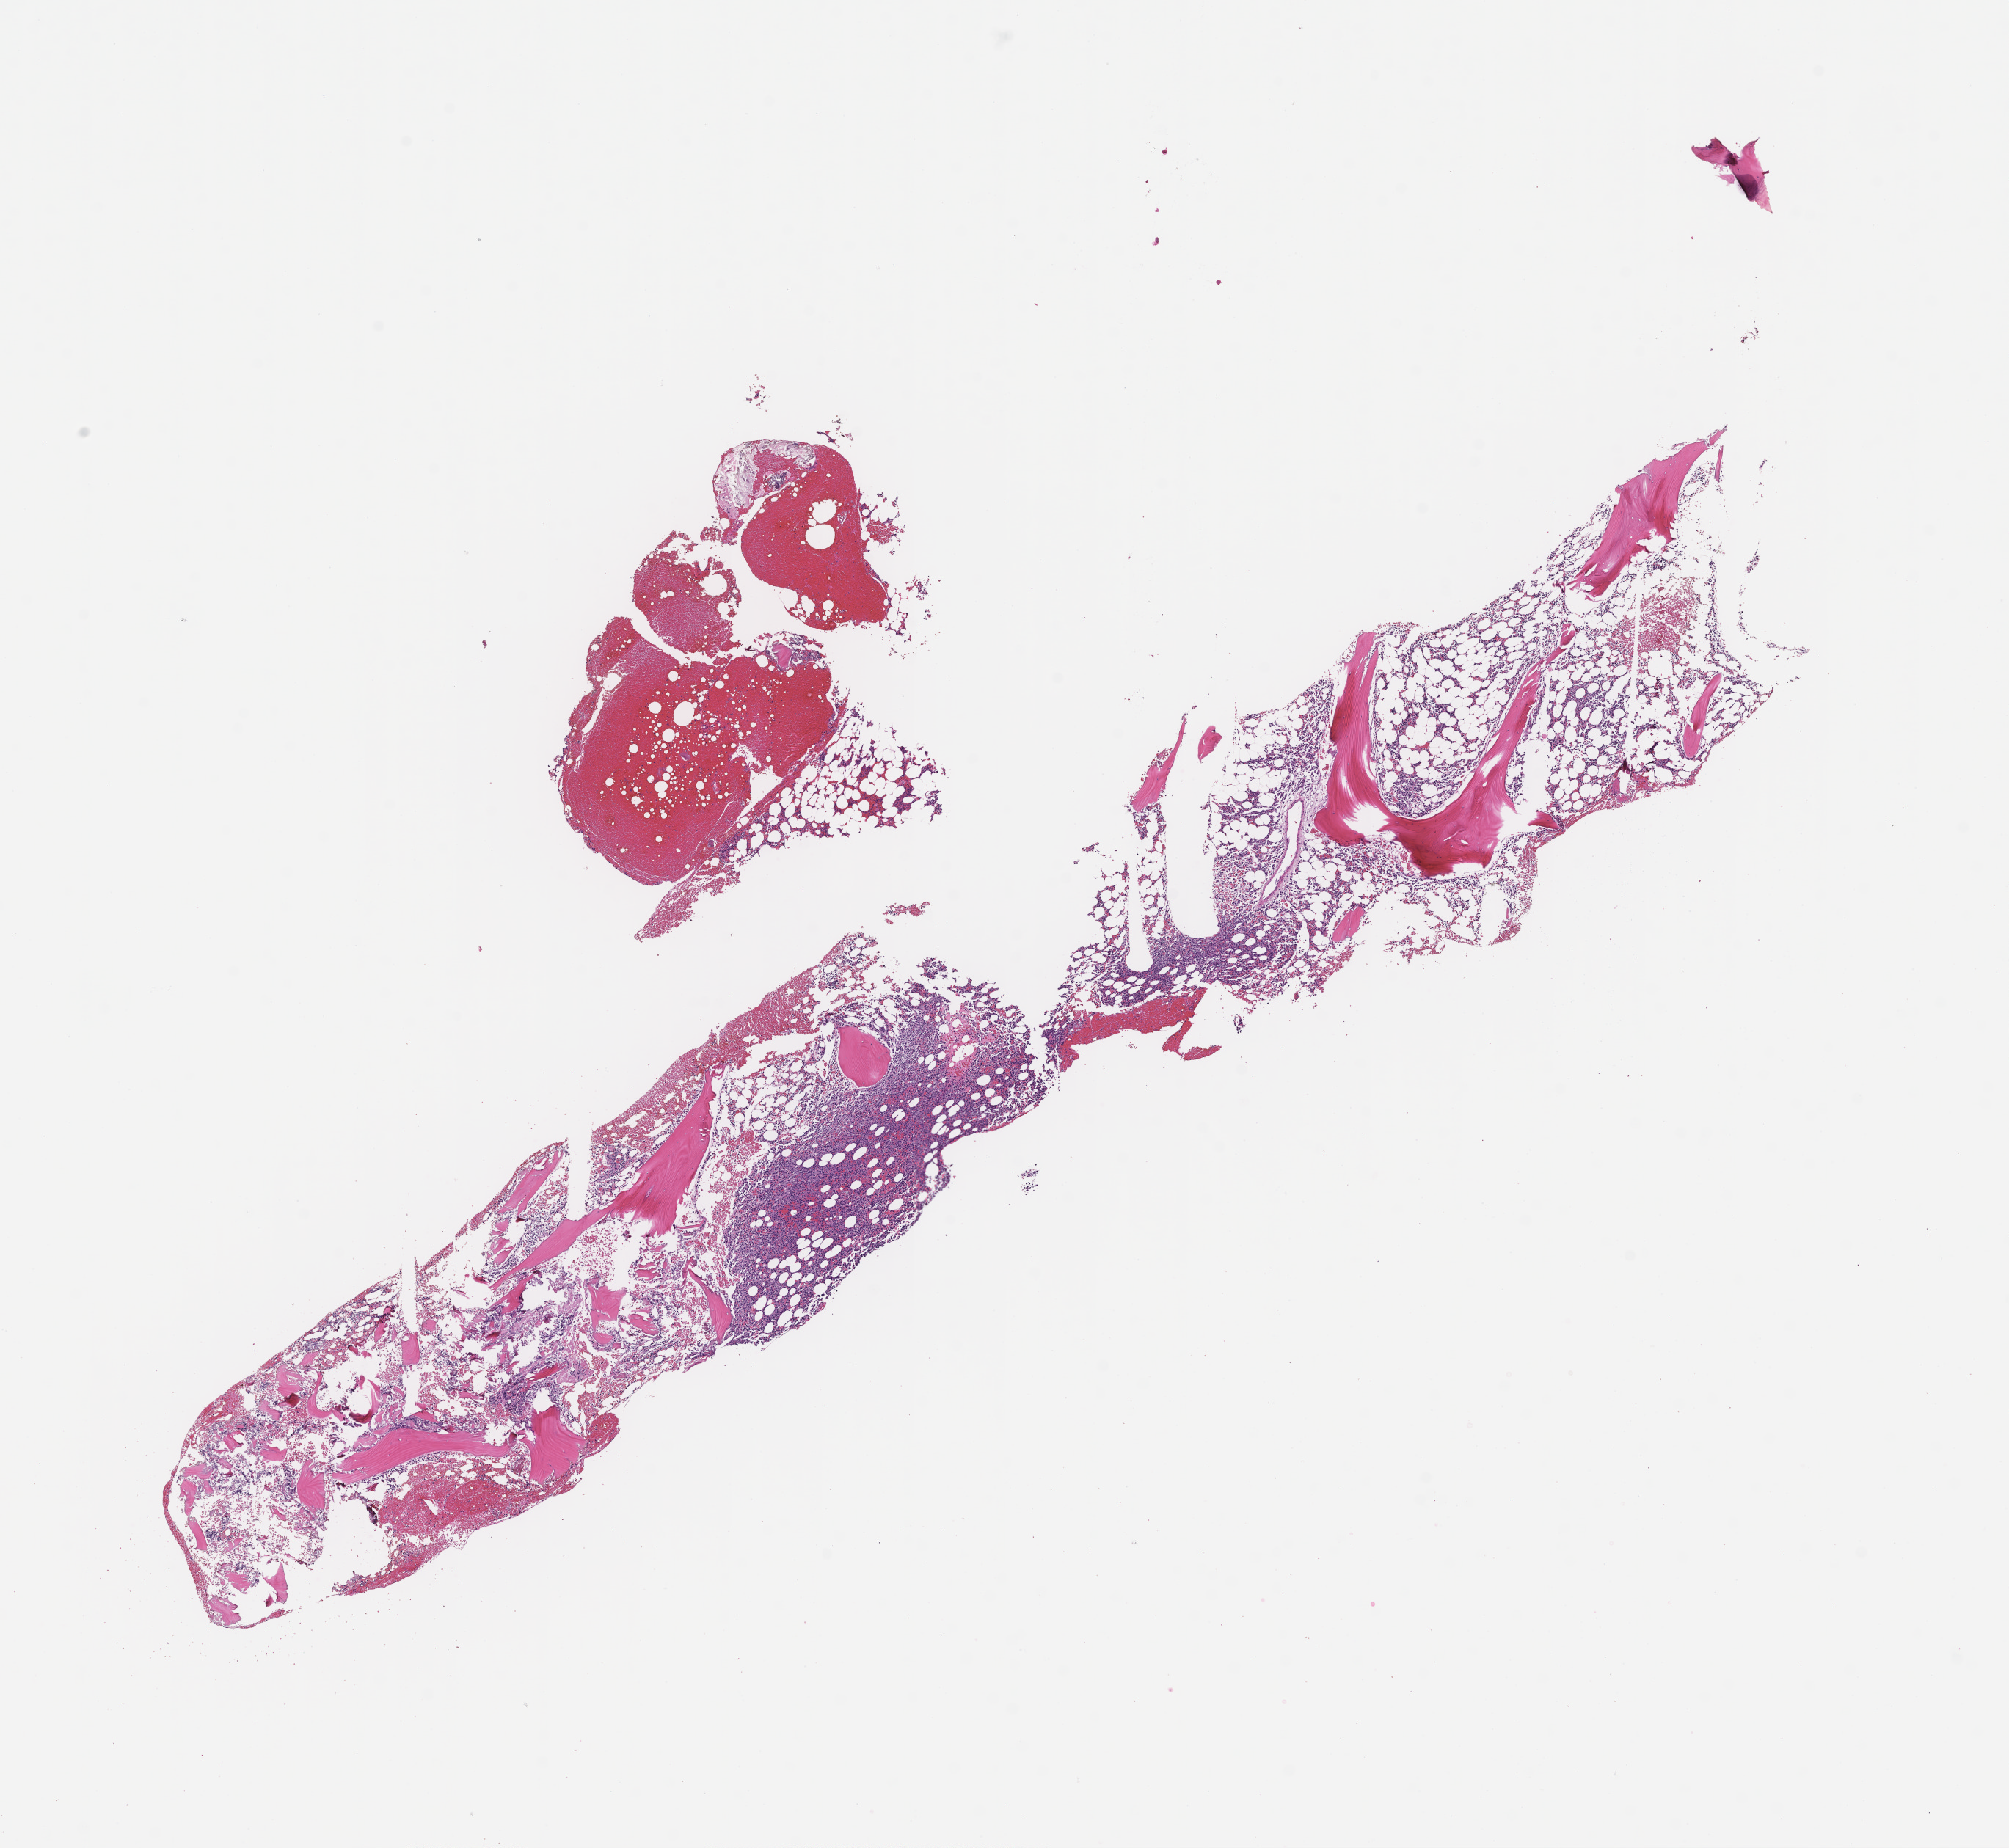
Whole-slide image, haematoxylin and eosin stain, a low-resolution overview of the entire scanned area, about 11.1 x 10.2 mm; FFPE section; site: bone marrow; collected at baseline (before treatment). Patient sex: female.
This section: primary tumour tissue. Diagnosis: Plasma Cell Myeloma.